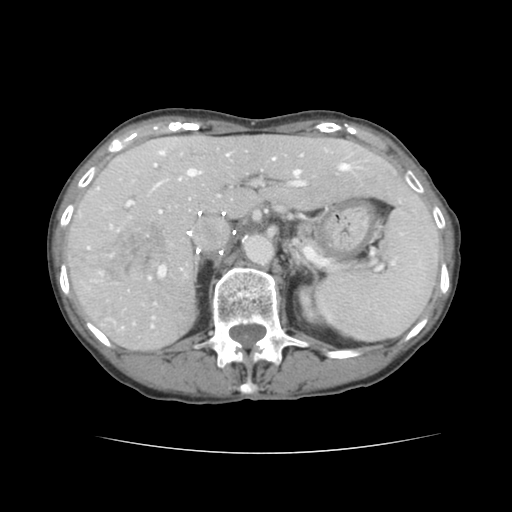
Contrast-enhanced abdominal CT, one axial slice. Position 92 of 136 along the scan axis. Intravenous contrast given. Soft-tissue window (W 400 / L 40 HU). 2.5 mm slice thickness. 512 × 512 image matrix. Female patient, age 77 years. Case-level facts recorded for this patient, not image findings: diagnosis: colorectal cancer liver metastases, imaged before liver resection; multiple liver metastases: yes; largest metastasis: 3 cm; disease in both lobes: no.
Annotated regions visible in this slice (expert manual segmentation):
- hepatic veins: bounding box <122,152,349,329> (left, top, right, bottom; pixels)
- liver: <68,136,426,350>
- planned liver remnant (the part of the liver to remain after resection): <153,136,425,216>
- portal vein (with intrahepatic branches): <98,151,308,280>
- liver metastasis: <106,223,169,281>